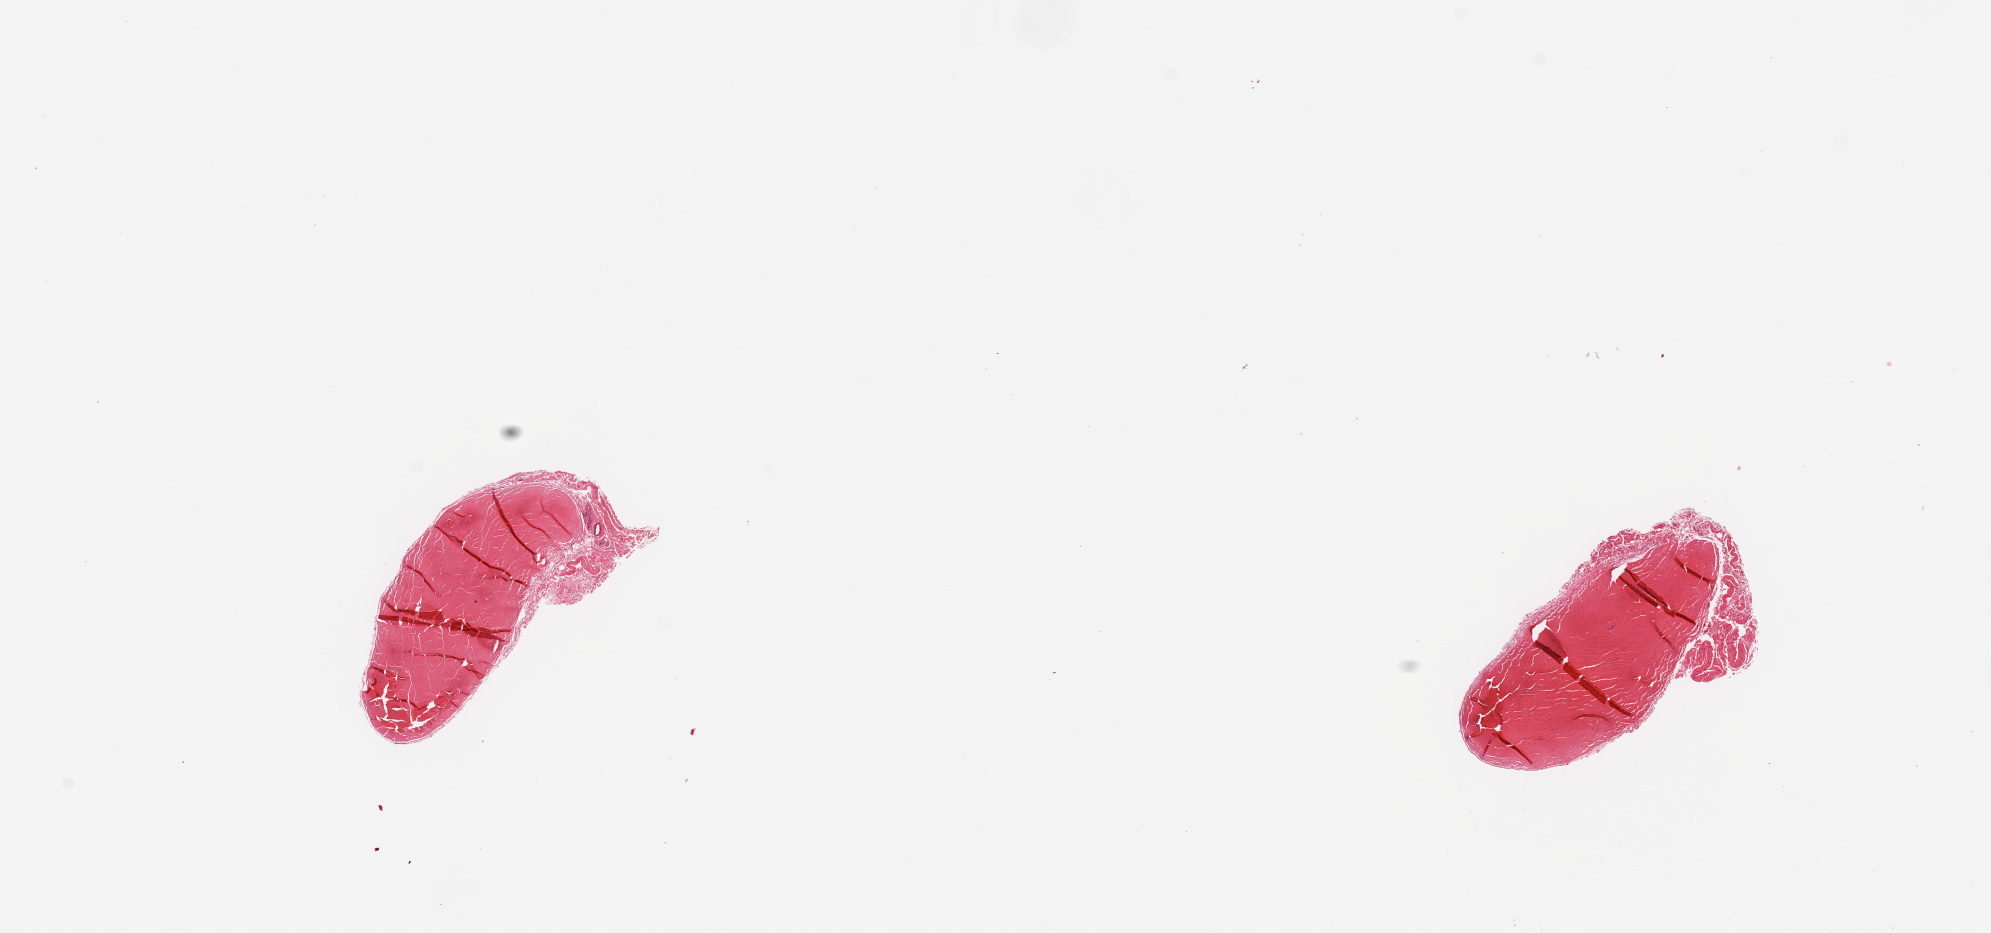
Whole-slide image, H&E stain, brightfield, a low-resolution overview of the entire scanned area, about 15.8 x 7.4 mm; PAXgene-fixed paraffin-embedded (PFPE) section; sampled site (target tissue): tibial nerve; donor tissue sample. Male donor.
Reviewer comment on this tissue sample: 2 pieces; tendon, not nerve.